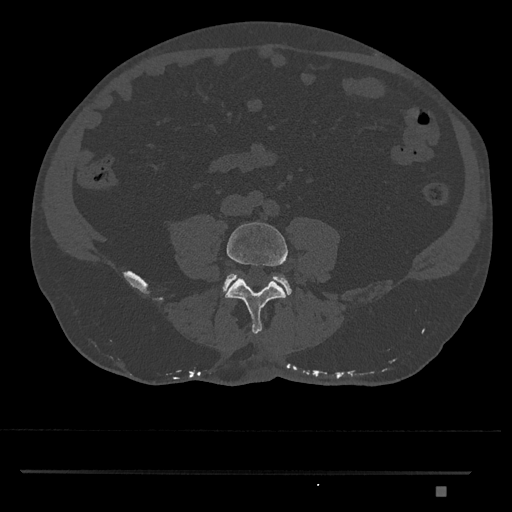
CT including the spine, one axial slice. Position 600 of 1134 along the scan axis. 120 kVp. Bone window (W 1800 / L 400 HU). 0.5 mm slice thickness. 512 × 512 image matrix, field of view 429 × 429 mm. Patient: male, 65 years. From the clinical record (not read from this slice): primary cancer: prostate.
Outlined on this slice (semi-automatic segmentation, software-assisted and operator-edited):
- L4 vertebra: box from (x=225, y=222) to (x=288, y=334) px
- L5 vertebra: (x=222, y=274)–(x=292, y=295)